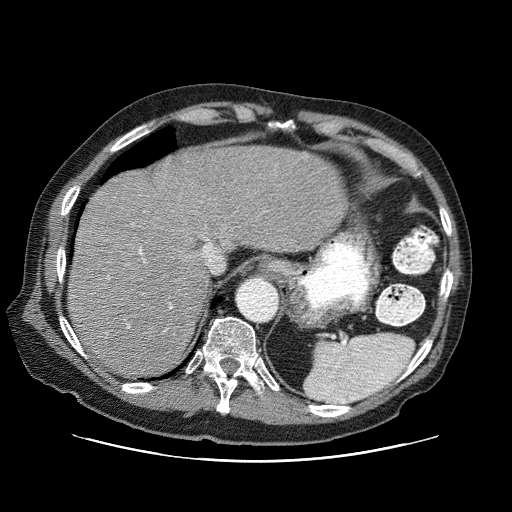
Contrast-enhanced abdominal CT (liver protocol), one axial slice; 120 kVp; one of 3 acquisitions stored at this slice position; soft-tissue window (W 400 / L 40 HU); 2.5 mm slice thickness; 512 × 512 image matrix, field of view 400 × 400 mm. From the clinical record (not read from this slice): diagnosis: hepatocellular carcinoma (patient treated with transarterial chemoembolisation; whether this scan precedes or follows treatment is not stated here); TNM stage (as recorded): Stage-IIIA; Child-Pugh class: A; tumour differentiation: well differentiated; tumour nodularity: multinodular.
Structures marked on this image (semi-automatic segmentation, software-assisted and operator-edited):
- liver parenchyma outside the tumour (the mass and vessels are separate outlines, so this box may not span the whole liver): bounding box (x1, y1, x2, y2) in pixels: (68, 146, 346, 376)
- liver vessels: (128, 239, 208, 331)